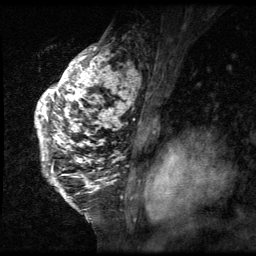
Breast MRI (dynamic contrast-enhanced), one sagittal slice; slice 43 of 64 in the series (ordered by position); 3 images stored at this slice position (order not interpretable as contrast timing); 1.5 T; TE 4.2 ms, TR 9 ms; 2.5 mm slice thickness; 256 × 256 image matrix, field of view 180 × 180 mm. Female patient, age 50 years. From the clinical record (not read from this slice): setting: breast cancer imaged before/during neoadjuvant chemotherapy; receptor status: triple-negative.
Structures marked on this image (semi-automatic segmentation, software-assisted and operator-edited):
- analysis volume of interest (the breast-tissue region the enhancement analysis was run in; not a lesion): box from (x=26, y=39) to (x=140, y=212) px
- tumour enhancement mask (voxels above the 140 % enhancement threshold inside the analysis volume of interest): (x=35, y=46)–(x=140, y=202)